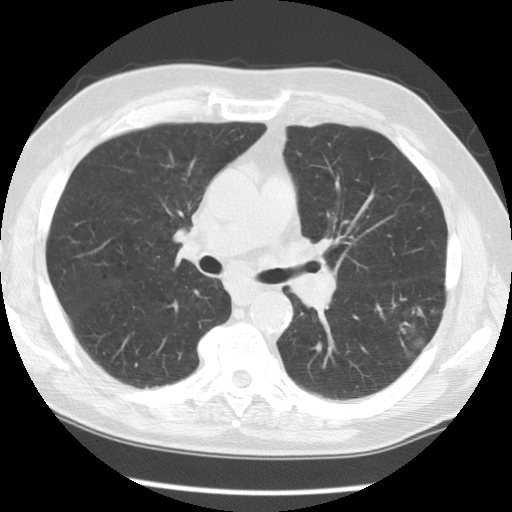
Low-dose screening chest CT, axial slice, baseline screening round, lung window (W 1500 / L -600 HU), 120 kVp, slice 51 of 130 in the series, 512 × 512 image matrix, field of view 340 × 340 mm. Male, age 71 years at enrolment. Former smoker at enrolment.
Lesion marked by an expert reader, bounding box [x1, y1, x2, y2] px = [373, 289, 456, 366]. The screening reader recorded 3 non-calcified nodules or masses ≥4 mm on this exam; which of them this box marks is not recorded. Official screen result: positive, change unspecified: nodule(s) >= 4 mm or enlarging nodule(s), mass(es), or other non-specific abnormalities suspicious for lung cancer. Lung cancer was diagnosed 42 days after this screen: small cell carcinoma, NOS, left lower lobe, poorly differentiated (G3), stage IIIA (AJCC 6th edition), 19 mm at pathology.